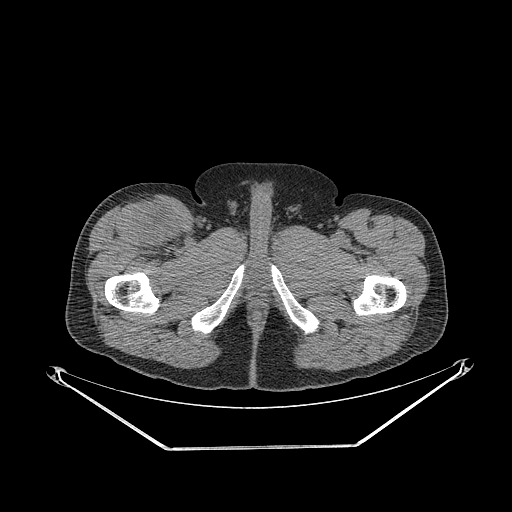
CT of an extremity soft-tissue mass (from a PET/CT study), one axial slice. Position 304 of 311 along the scan axis. Reconstruction kernel STANDARD. 140 kVp. Soft-tissue window (W 400 / L 40 HU). 3.75 mm slice thickness. 512 × 512 image matrix, field of view 500 × 500 mm. Male patient. From the clinical record (not read from this slice): histological type: pleiomorphic leiomyosarcoma; grade: intermediate; site of the primary tumour: right thigh.
Outlined on this slice (expert contour drawn on MRI and transferred to this co-registered scan by the dataset authors):
- gross tumour volume including surrounding oedema: bounding box [x1, y1, x2, y2] px = [135, 201, 181, 248]
- gross tumour volume (mass): [142, 210, 179, 247]